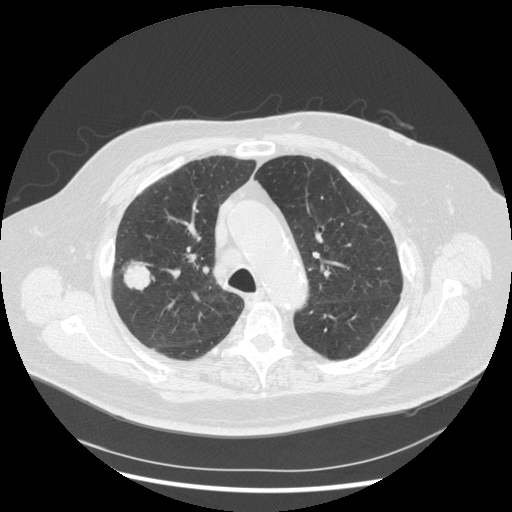
Low-dose screening chest CT, one axial slice. Position 201 of 263 along the scan axis. 120 kVp. Lung window (W 1500 / L -600 HU). 2.5 mm slice thickness. 512 × 512 image matrix, field of view 400 × 400 mm.
Structures marked on this image (manually delineated by an expert):
- lesion 1 (tumor, upper lobe of right lung): bounding box (x1, y1, x2, y2) in pixels: (124, 264, 154, 290)